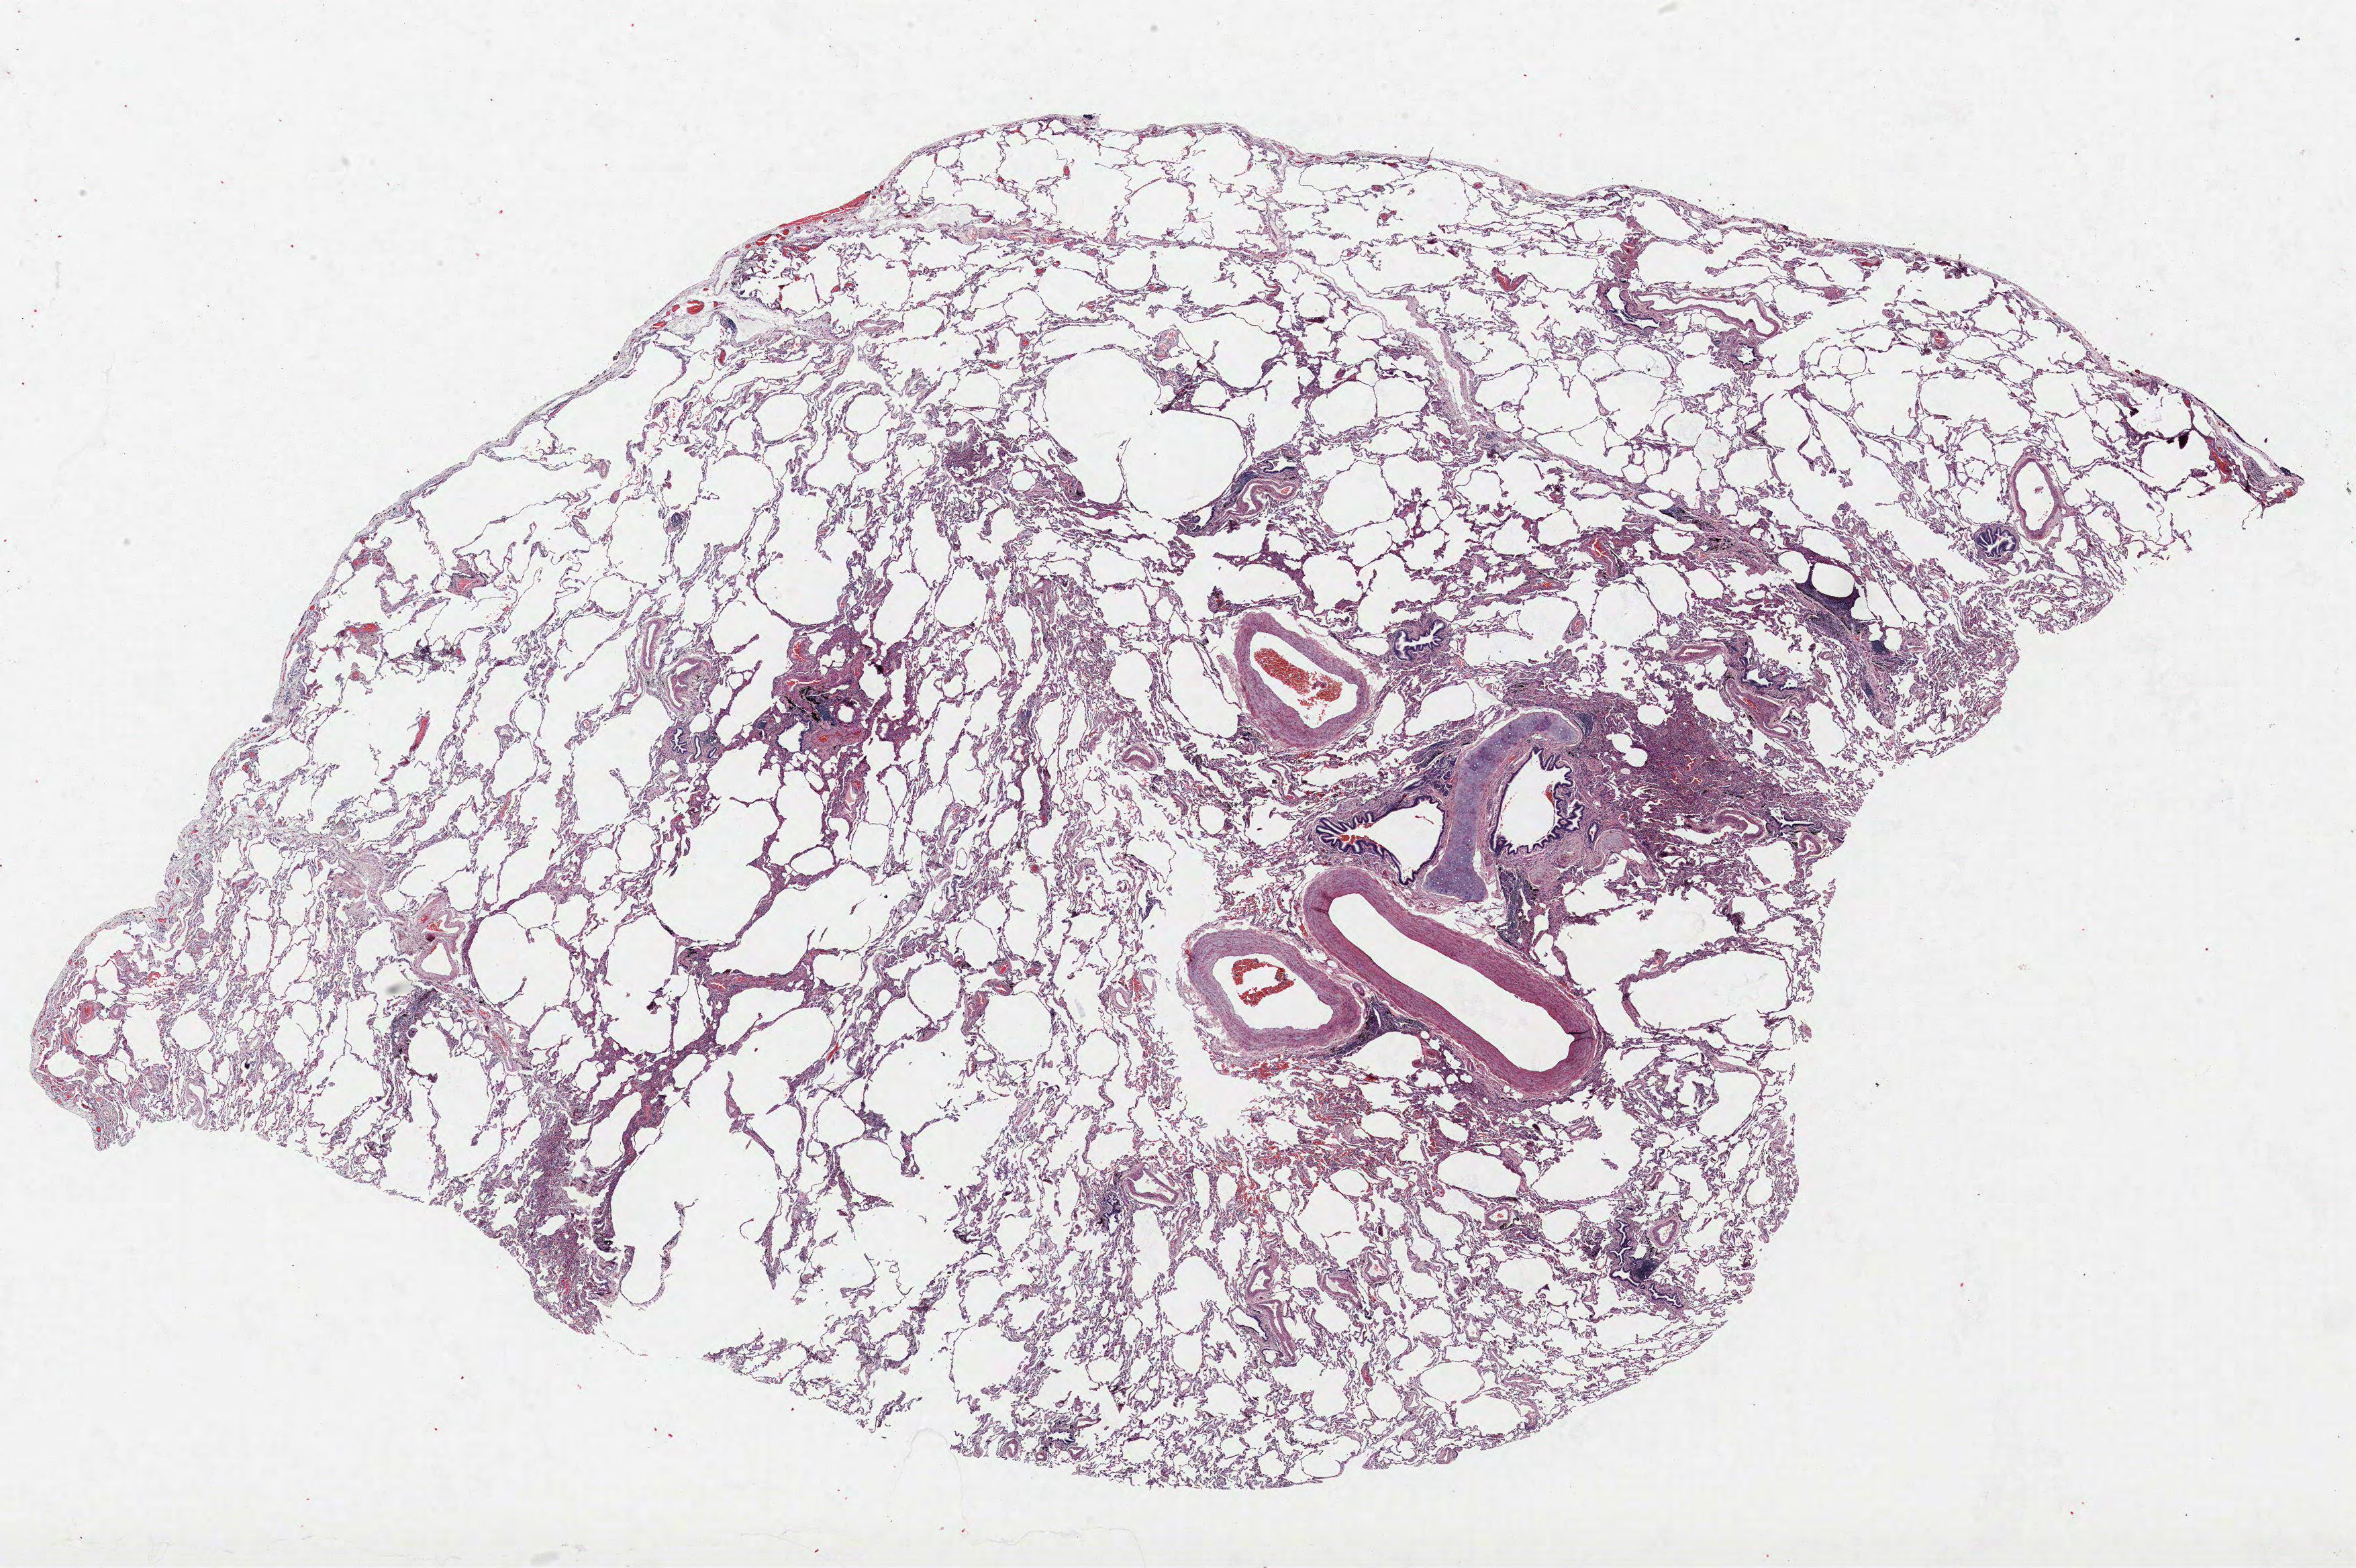
H&E-stained whole-slide image — low-resolution overview of the scanned area, about 28.1 x 18.7 mm (acquisition: 40x scan), formalin-fixed paraffin-embedded (FFPE) section, lung tissue. Male, age 73 at enrolment. Current smoker at enrolment. Grade: poorly differentiated (G3).
Stage (AJCC 6th edition): IA. Participant's lung-cancer diagnosis: Neuroendocrine carcinoma, NOS (ICD-O-3 8246/3). Tumour size (pathology): 26 mm. Primary tumour location (clinical record): left upper lobe.